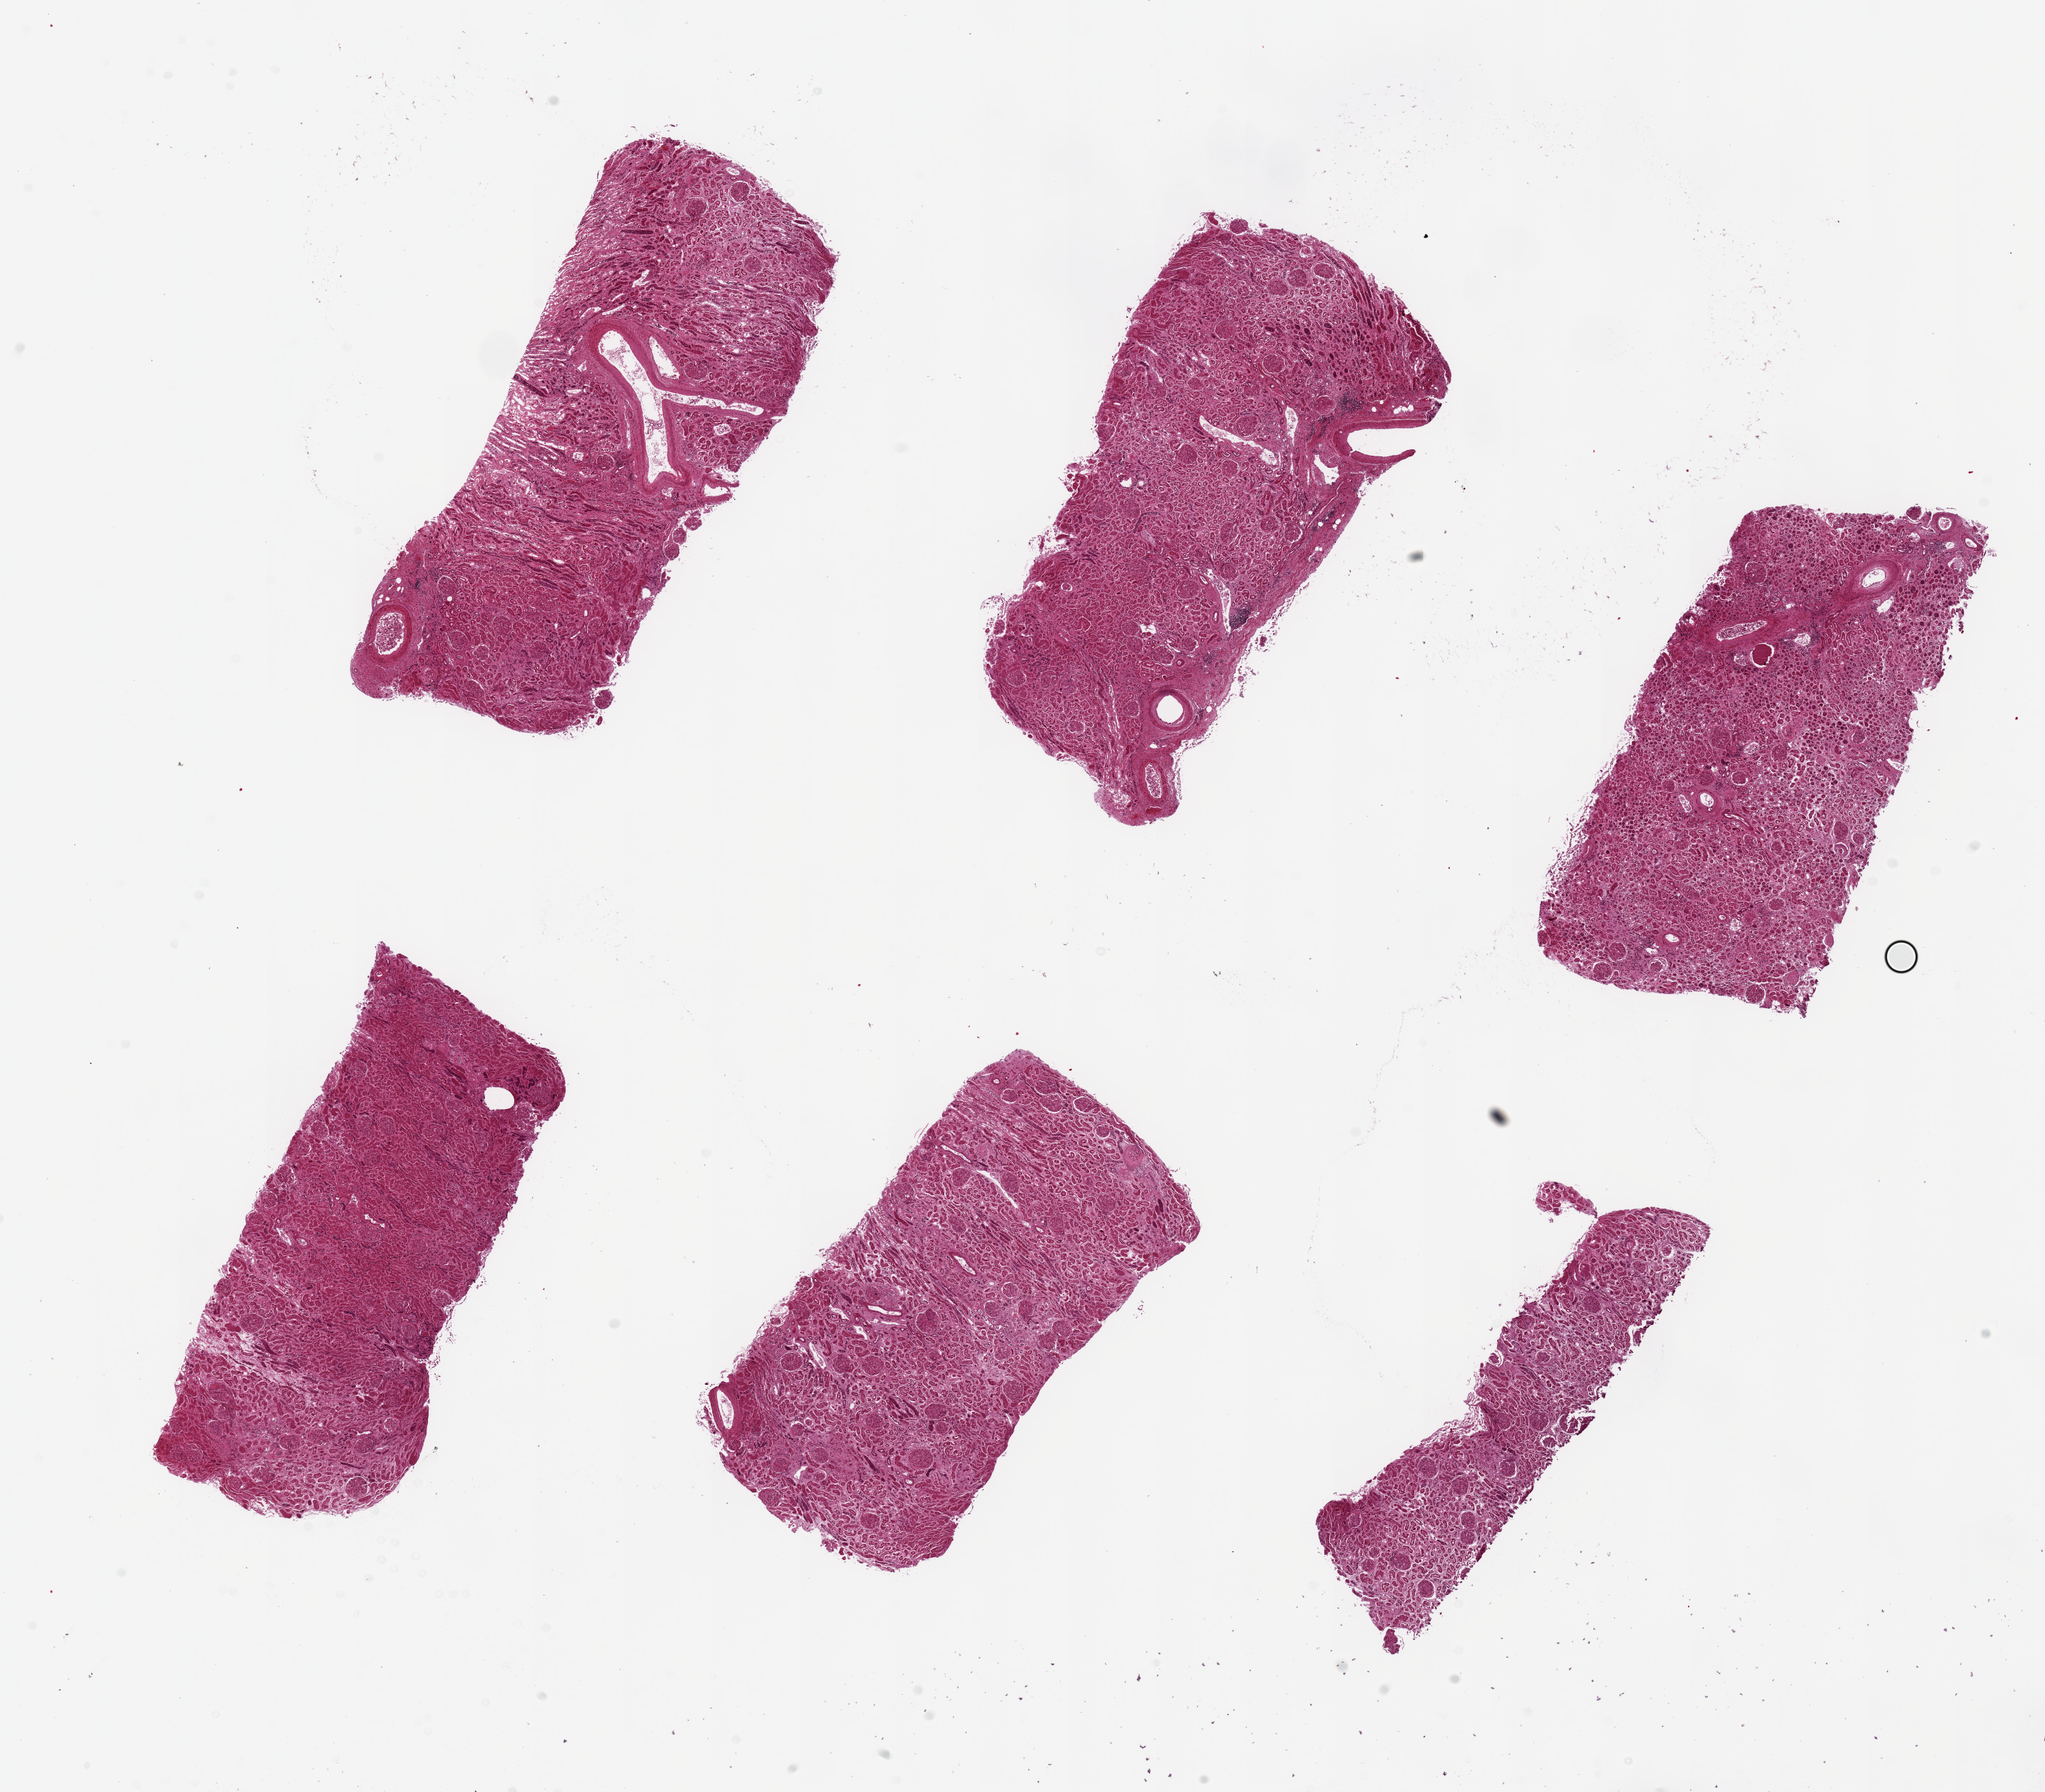
Whole-slide image, hematoxylin and eosin (H&E) stain, brightfield, whole scanned area (about 22.6 x 19.8 mm) shown as a low-resolution overview, PAXgene-fixed paraffin-embedded (PFPE) section, section of renal cortex (target tissue), tissue donor sample. Donor sex: female.
Review note (as recorded): 6 pieces, up to 7x3mm; scattered arteriolar and glomerular sclerosis (hypertensive?).